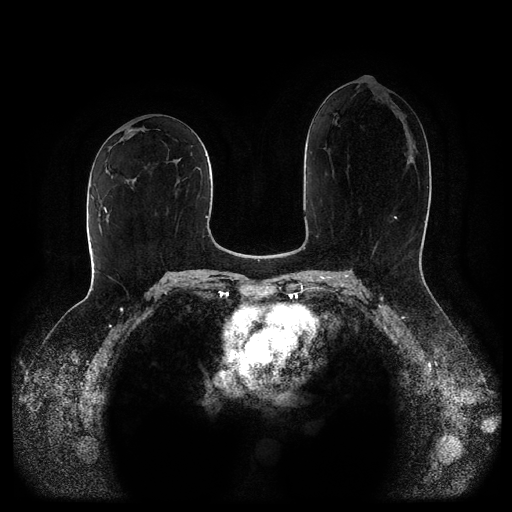
Breast MRI (dynamic contrast-enhanced, multi-phase), one axial slice. Dynamic contrast-enhanced series, time point 2 of 5 at this slice position (early post-contrast). 1.5 T. TE 2.6 ms, TR 5.2 ms. 512 × 512 image matrix, field of view 380 × 380 mm. Female patient, age 52 years.
Annotated regions visible in this slice (semi-automatically segmented with operator editing):
- breast lesion (labelled 'tumour' in the annotation; benign lesions carry a separate 'benign' label): box from (x=167, y=158) to (x=182, y=163) px